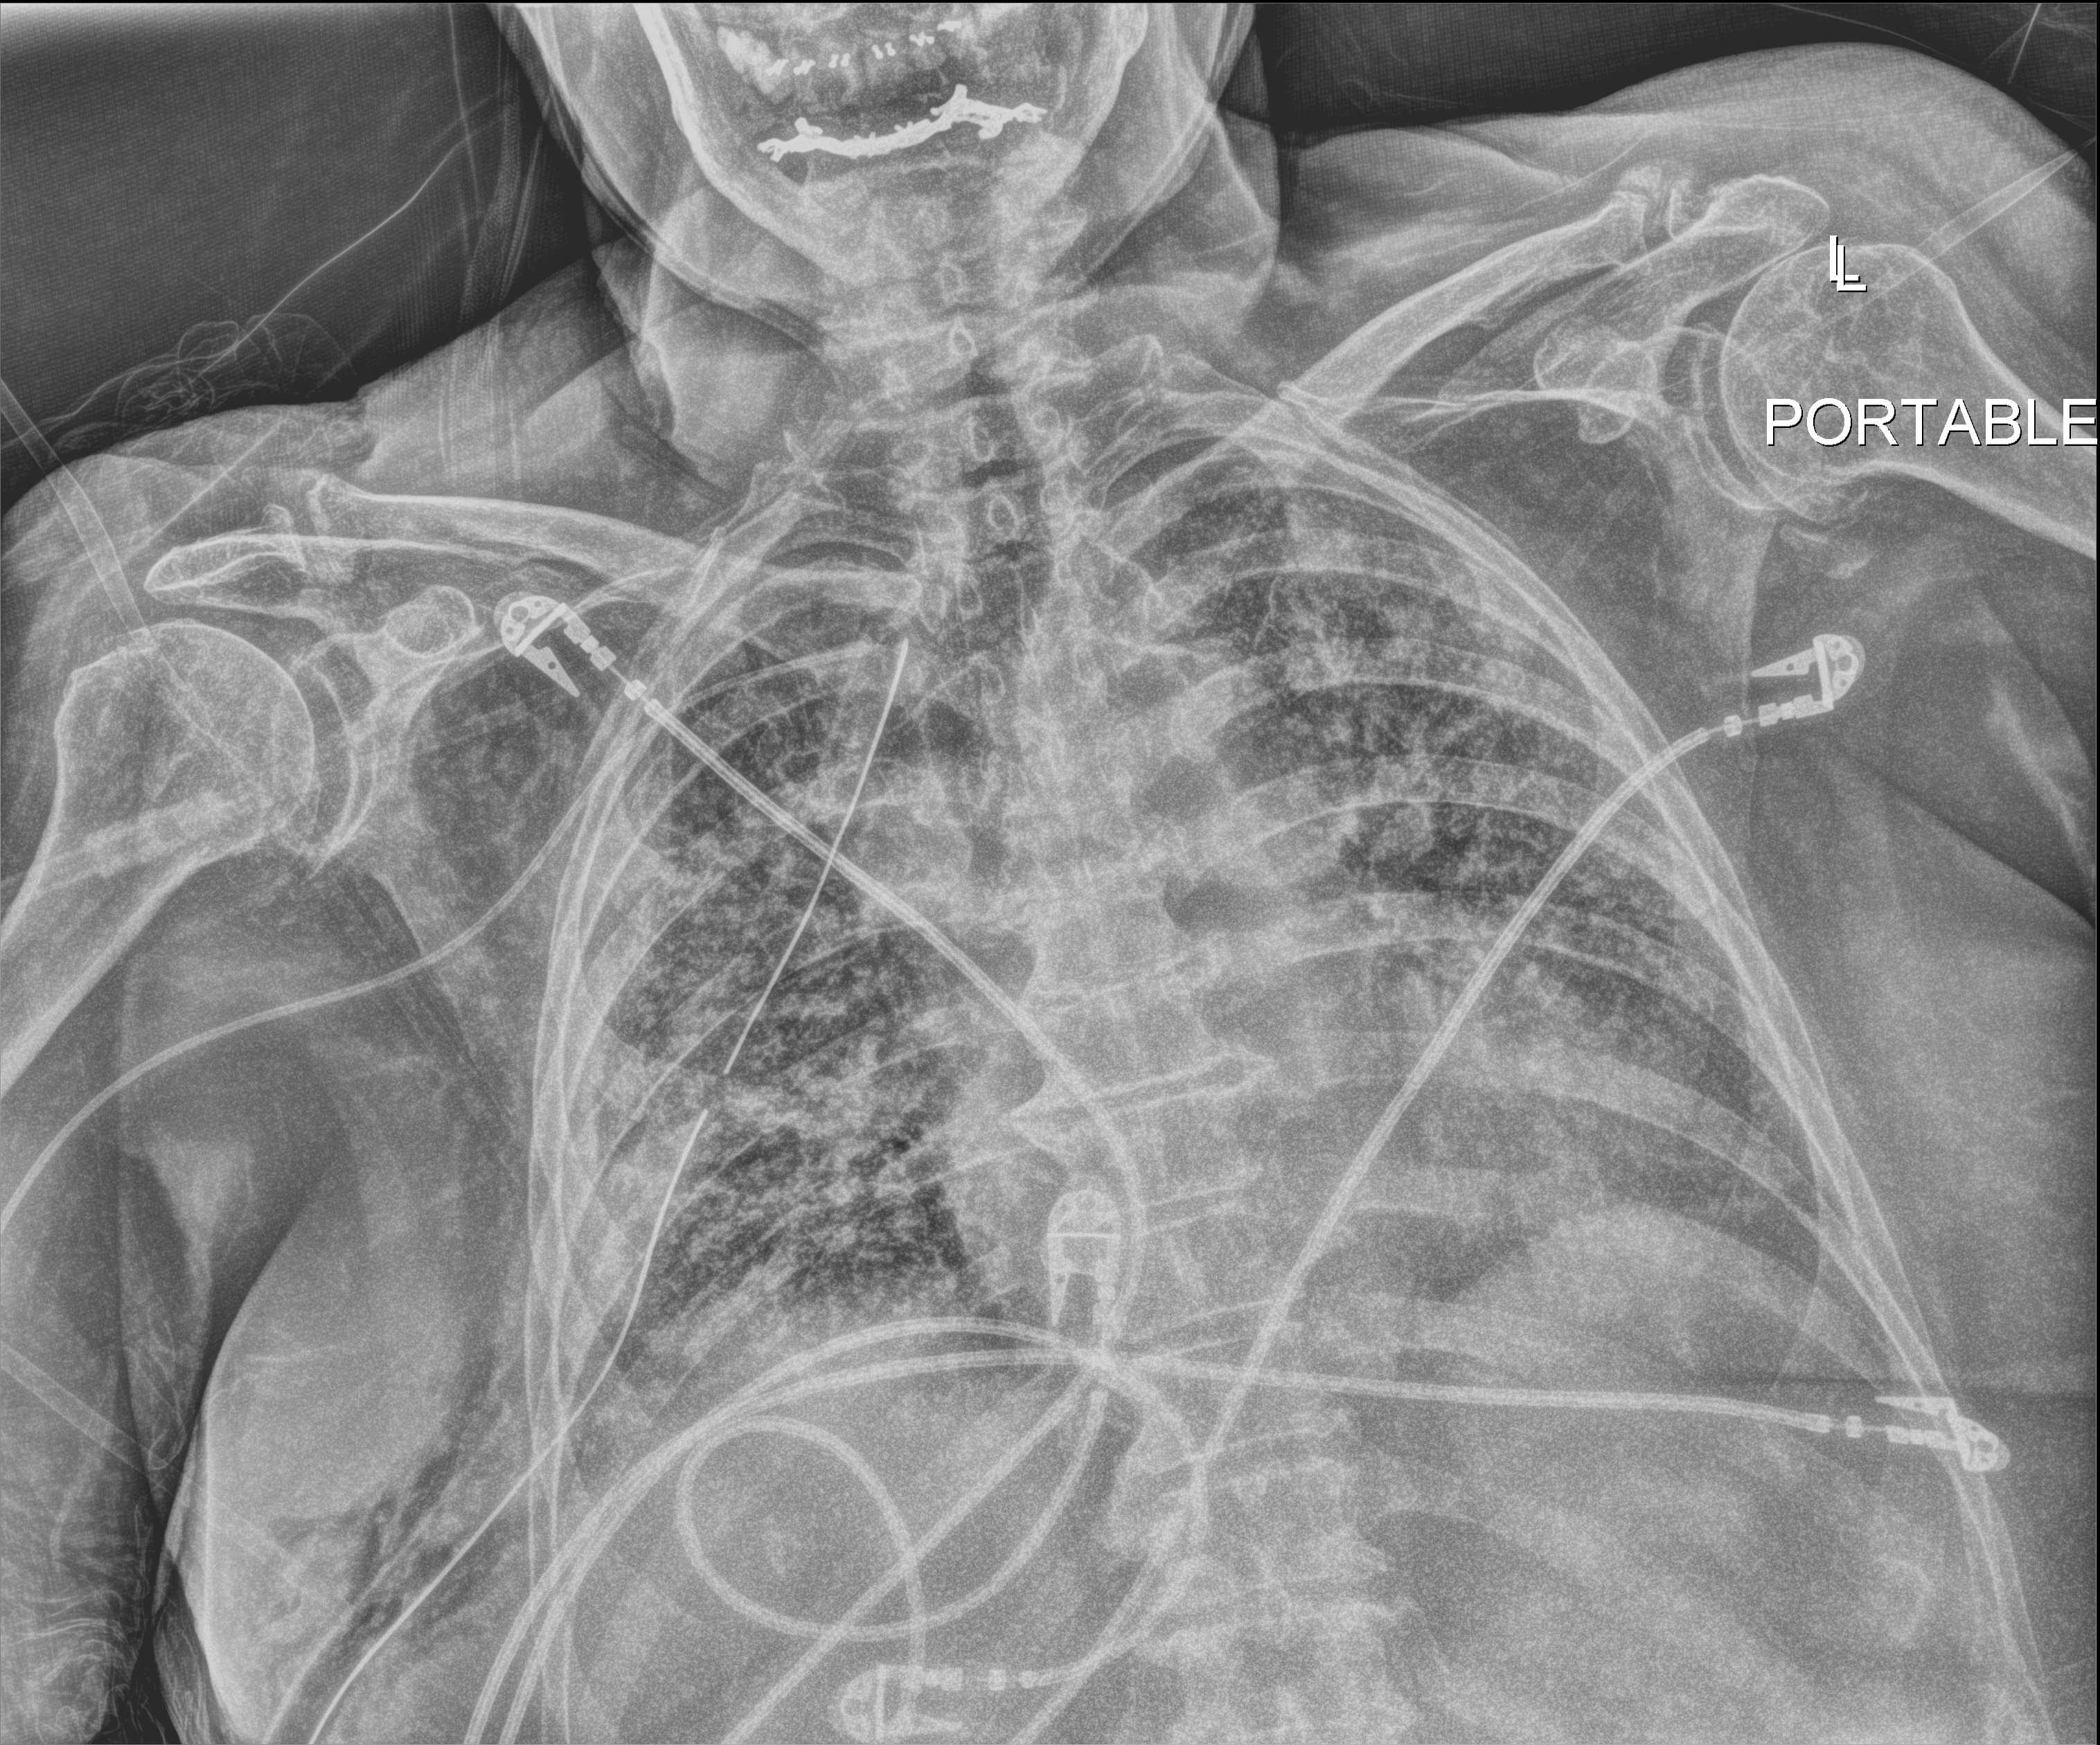
Chest X-ray (portable), anteroposterior (AP) projection. Patient hospitalised with COVID-19; female, aged 75–90 years.
From the hospital-stay record, not from the radiograph (when in the stay this image was taken is not recorded):
- mechanically ventilated during this hospital stay: yes
- hypertension (admission record): no